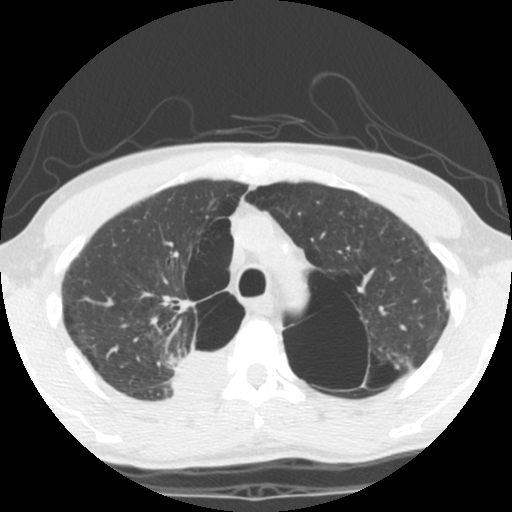
Chest CT (low-dose screening protocol), one axial image. Second annual screen. Lung window (W 1500 / L -600 HU). 2.5 mm slice thickness. Standard (soft-tissue) reconstruction kernel (STANDARD). Male, age 62 years at enrolment. Current smoker at enrolment.
- Expert-annotated lung lesion, box from (x=130, y=326) to (x=227, y=404) px.
- The exam's reader record, not a measurement of the box and not confirmed to be the same lesion: non-calcified nodule or mass ≥4 mm, 35 × 25 mm, soft tissue attenuation.
- Participant outcome: lung cancer diagnosed 14 days after this screen — non-small cell carcinoma, right upper lobe, poorly differentiated (G3), stage IA (AJCC 6th edition), 70 mm at pathology.